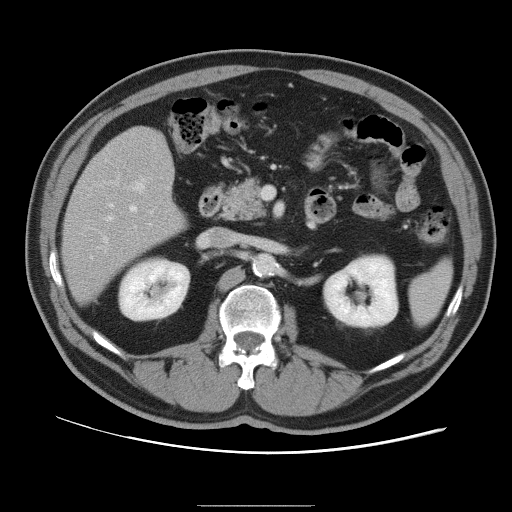
Contrast-enhanced abdominal CT, one axial slice; slice 47 of 105 in the series (ordered by position); 120 kVp; intravenous contrast given; soft-tissue window (W 400 / L 40 HU); 5 mm slice thickness; 512 × 512 image matrix, field of view 399 × 399 mm. Male patient, age 64 years. Case-level facts recorded for this patient, not image findings: diagnosis: colorectal cancer liver metastases, imaged before liver resection; multiple liver metastases: yes; largest metastasis: 3 cm; disease in both lobes: yes.
Annotated regions visible in this slice (expert manual segmentation):
- hepatic veins: bounding box <90,204,150,259> (left, top, right, bottom; pixels)
- liver: <63,128,185,303>
- planned liver remnant (the part of the liver to remain after resection): <65,129,185,303>
- portal vein (with intrahepatic branches): <104,178,145,242>